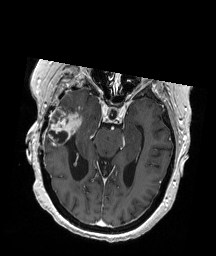
Brain MRI from a brain-tumour surgery series, one axial slice. Slice 119 of 192 in the series (ordered by position). T1-weighted post-contrast. 216 × 256 image matrix, field of view 211 × 250 mm. From the clinical record (not read from this slice): histopathology: Glioblastoma; WHO grade: 4; IDH mutation: no; tumour location: Right Temporal.
Structures marked on this image (outlined manually by an expert reader):
- tumour: bounding box [x1, y1, x2, y2] px = [48, 112, 83, 146]